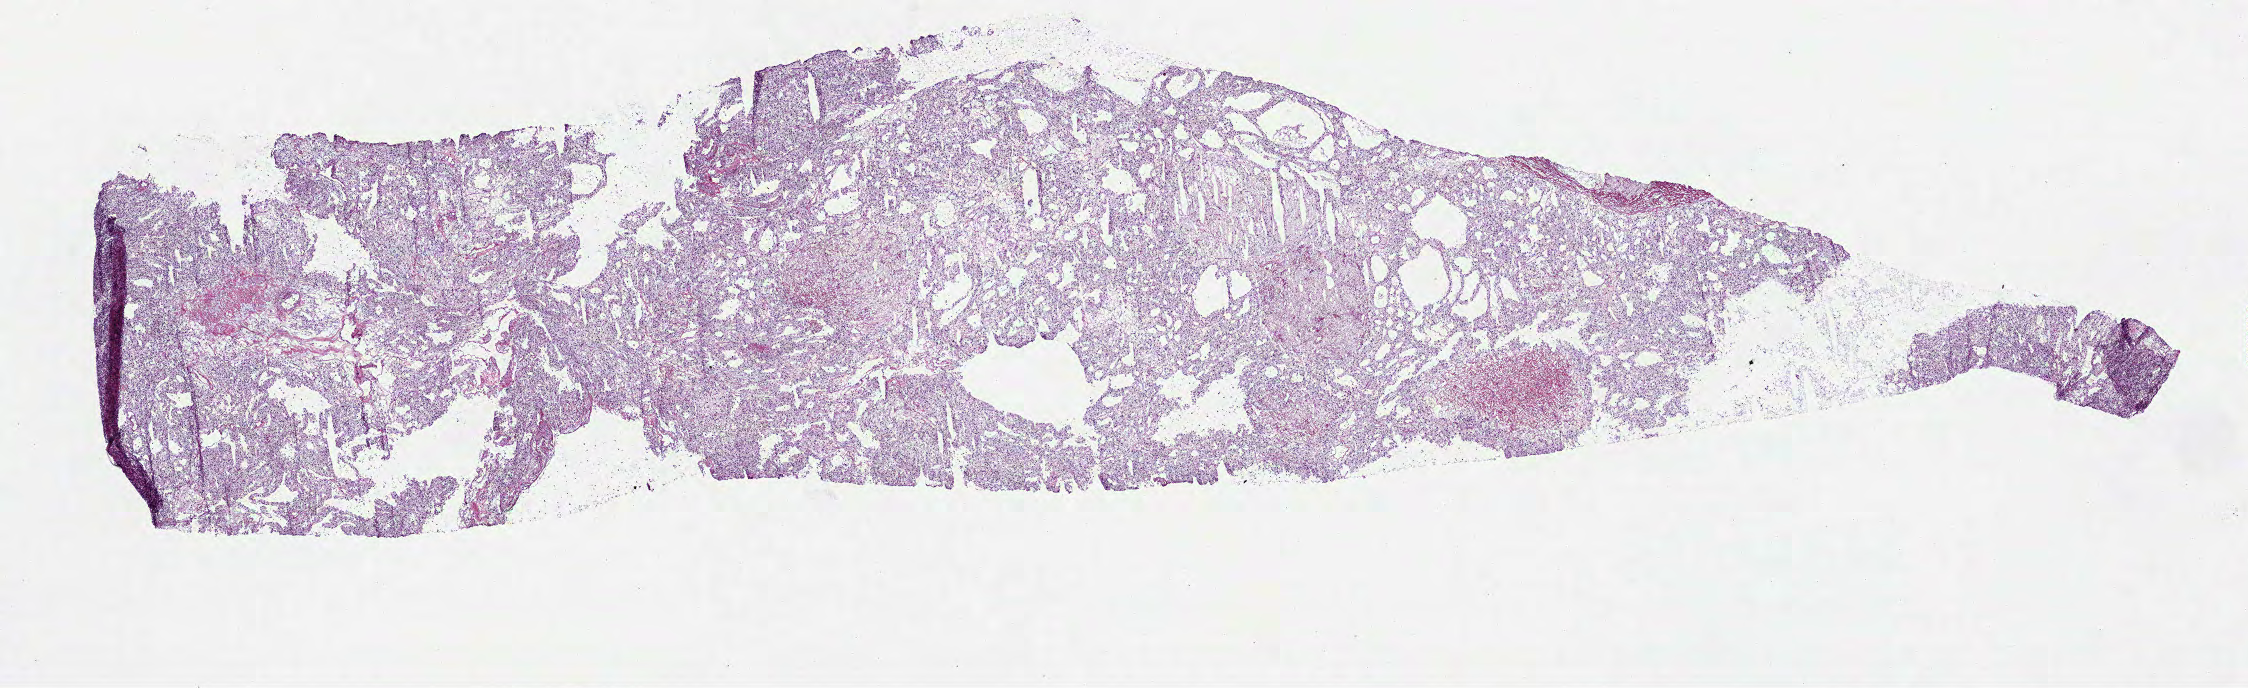
Hematoxylin and eosin (H&E) stained whole-slide image — whole scanned area (about 18.1 x 5.5 mm, slide scanned at 40x) shown as a low-resolution overview; frozen section from the top of the tissue portion; primary tumour sample from the kidney. Female patient; age at initial diagnosis 67 years. Histologic grade: G3 (poorly differentiated). Composition of this section per pathologist review: tumour cells 90%, tumour nuclei 85%, normal cells 0%, stromal cells 10%, necrosis 0%.
Diagnosis: Clear cell adenocarcinoma, NOS. AJCC pathologic stage: I. Laterality: right.